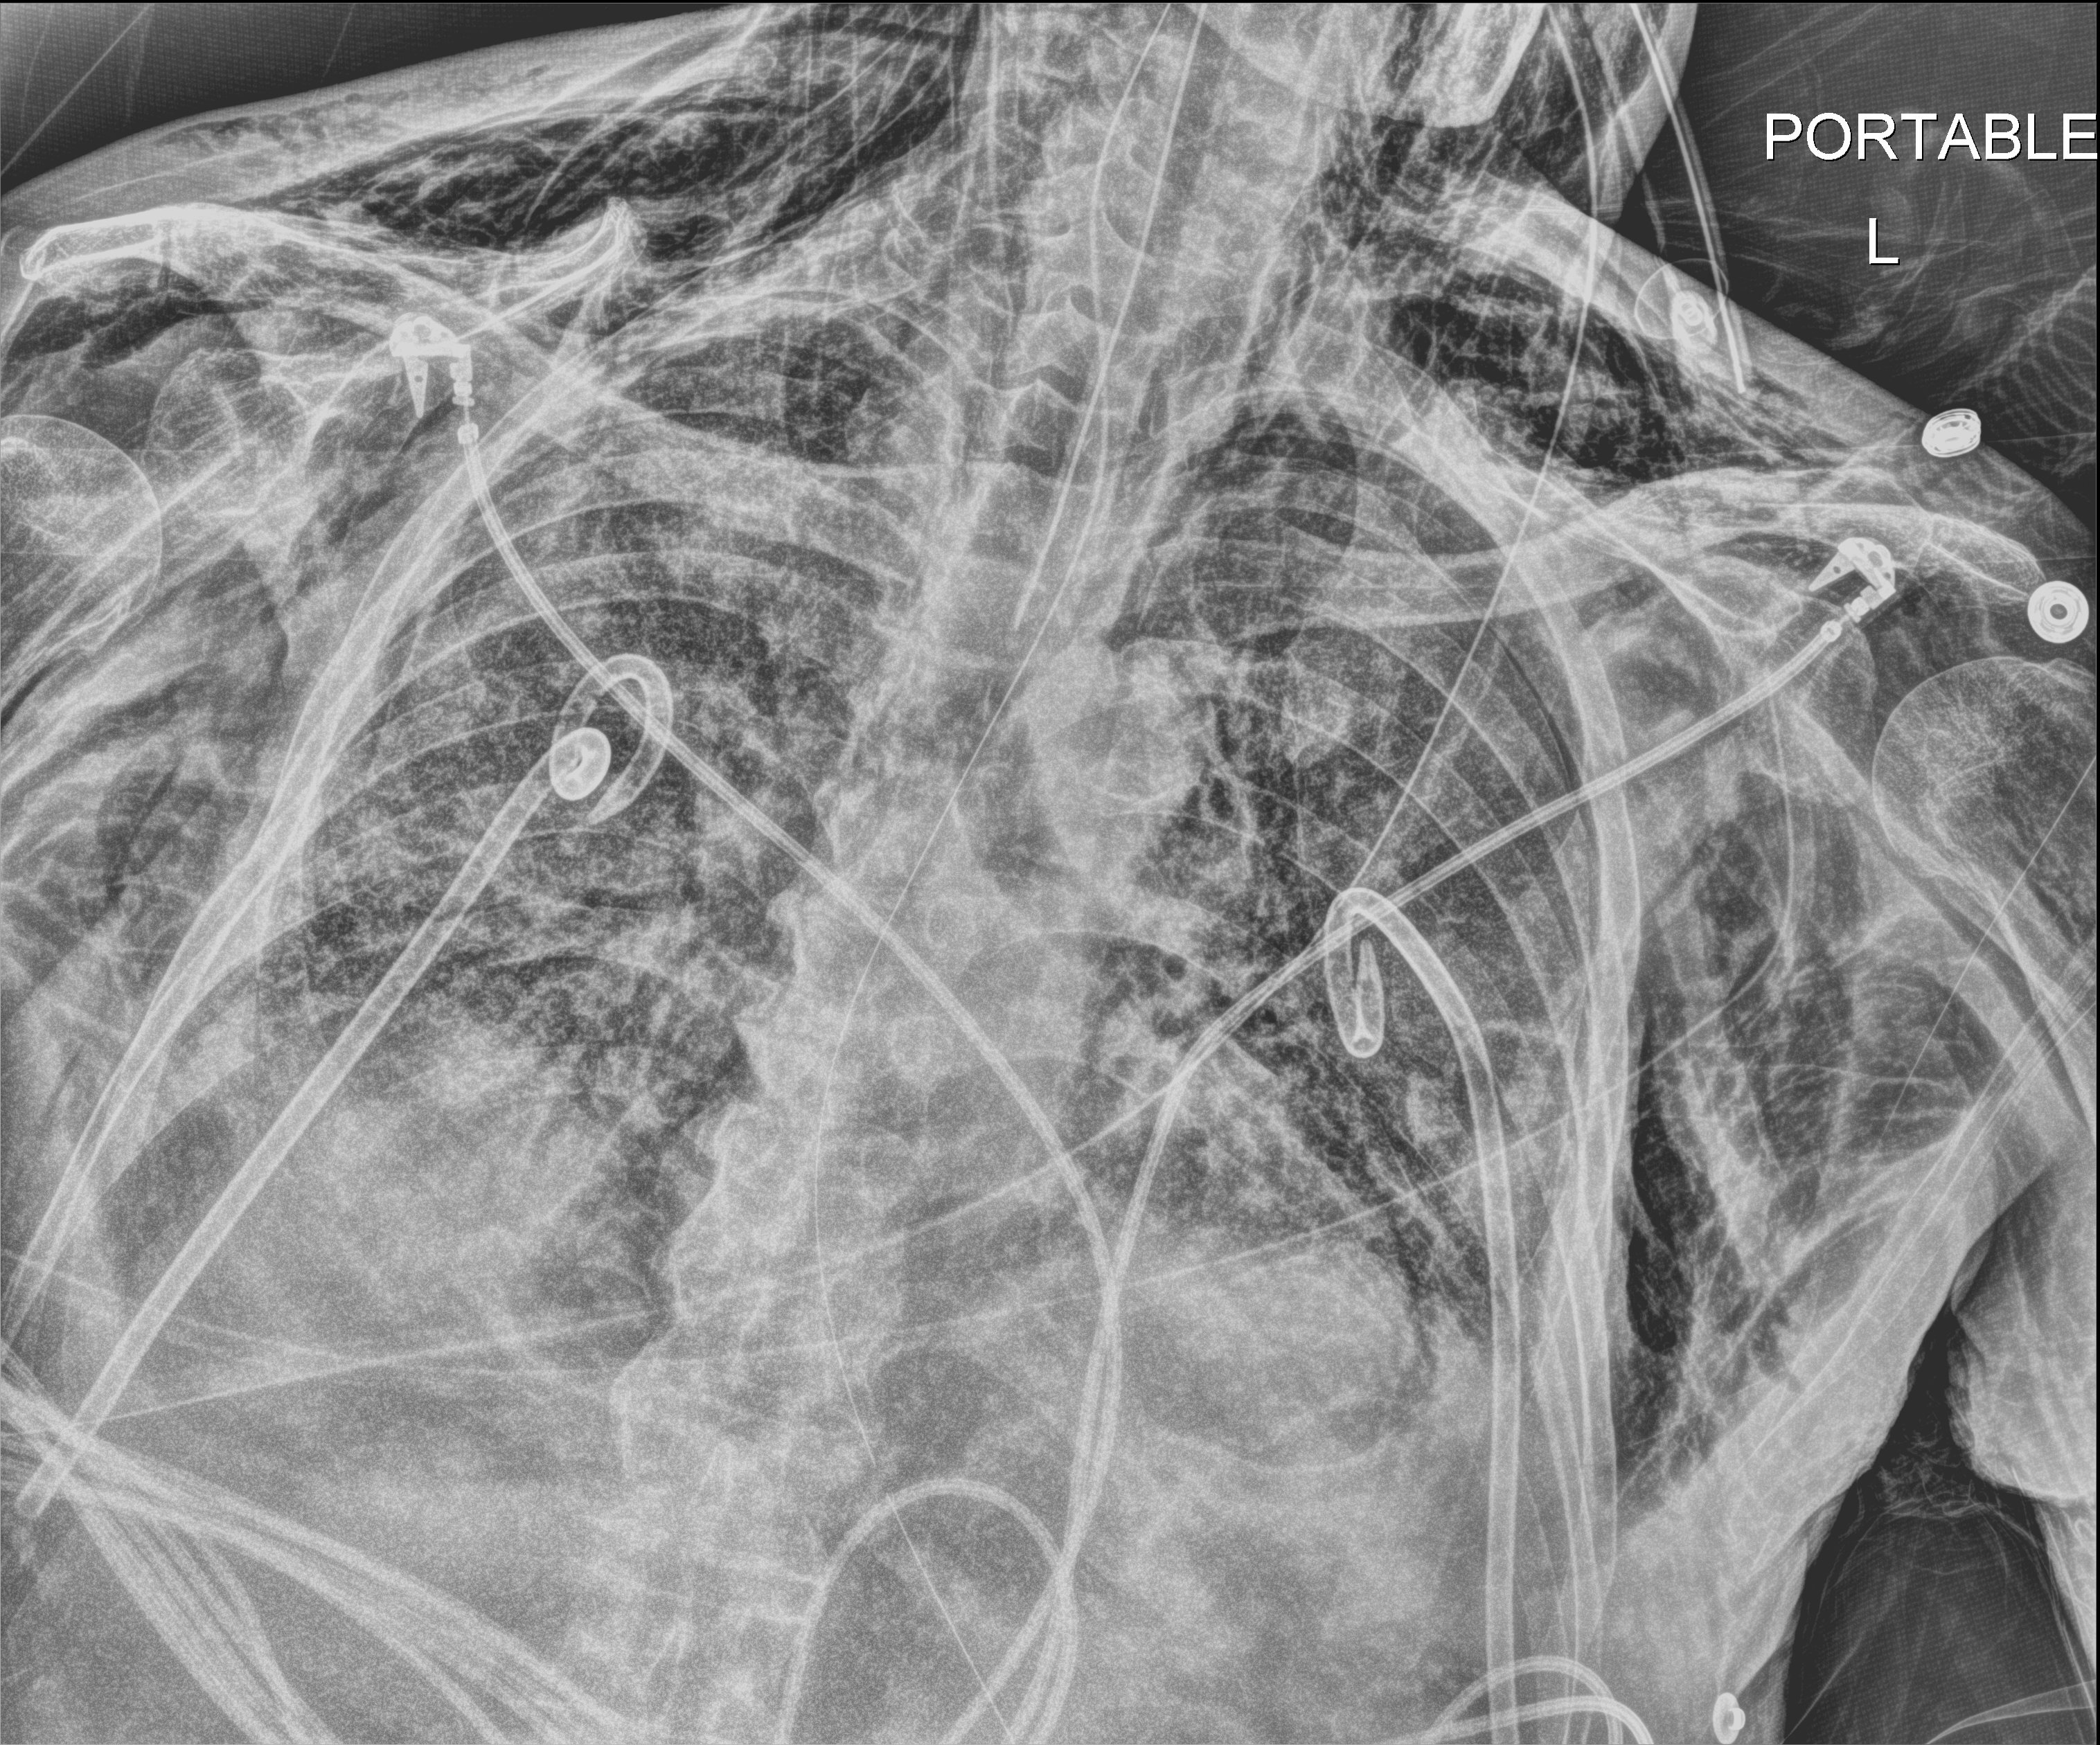
Chest X-ray (portable), anteroposterior (AP) projection. Patient hospitalised with COVID-19; male, aged 75–90 years.
Hospital-stay facts (about this admission, not read from this image; timing relative to this image not recorded):
- admitted to intensive care during this hospital stay: yes
- diabetes (admission record): no